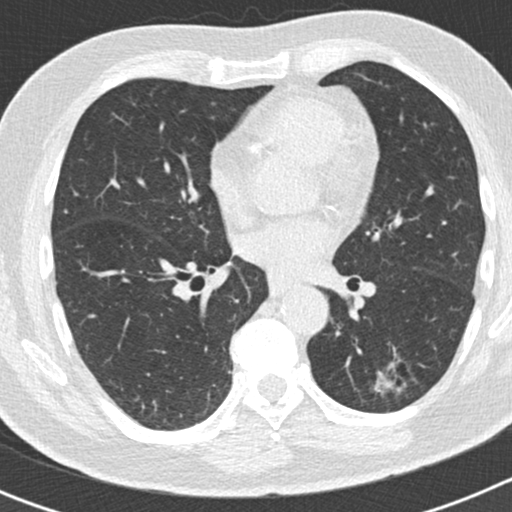
Axial slice from a low-dose chest CT screening exam. Second annual screen. Lung window (W 1500 / L -600 HU). 120 kVp. Male participant, aged 66 years at enrolment. Former smoker at enrolment.
Expert reader's lesion annotation, bounding box (x1, y1, x2, y2) in pixels: (352, 339, 412, 408). Screening reader's record for this exam (one nodule recorded; not confirmed to be the boxed lesion): non-calcified nodule or mass ≥4 mm, left lower lobe, 50 × 33 mm, smooth margins, pre-existing on the prior screen: yes; interval growth: yes. Official screen result: positive, other. Participant outcome: lung cancer diagnosed 440 days after this screen — adenocarcinoma, NOS, left lower lobe, poorly differentiated (G3), stage IB (AJCC 6th edition), 38 mm at pathology.